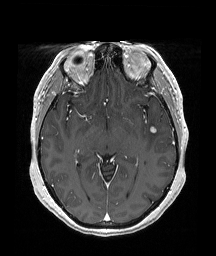
Brain MRI from a brain-tumour surgery series, one axial slice; position 110 of 192 along the scan axis; T1-weighted post-contrast; 216 × 256 image matrix, field of view 211 × 250 mm. From the clinical record (not read from this slice): histopathology: Papillary glioneuronal tumor; WHO grade: 1; tumour location: Left Temporal.
Outlined on this slice (outlined manually by an expert reader):
- tumour: box from (x=150, y=127) to (x=156, y=132) px